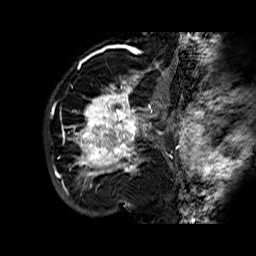
Breast MRI (dynamic contrast-enhanced), one sagittal slice. Position 46 of 60 along the scan axis. Dynamic contrast-enhanced series, time point 2 of 6 at this slice position (early post-contrast). 1.5 T. TE 6.3 ms, TR 32.4 ms. 4 mm slice thickness. 256 × 256 image matrix. Female patient. From the clinical record (not read from this slice): setting: breast cancer imaged before/during neoadjuvant chemotherapy; receptor status: HR-positive, HER2-negative.
Annotated regions visible in this slice (semi-automatic segmentation, software-assisted and operator-edited):
- analysis volume of interest (the breast-tissue region the enhancement analysis was run in; not a lesion): bounding box [x1, y1, x2, y2] px = [68, 72, 177, 183]
- tumour enhancement mask (voxels above the 100 % enhancement threshold inside the analysis volume of interest): [70, 72, 177, 182]